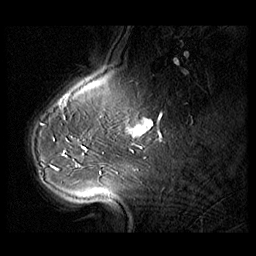
Breast MRI (dynamic contrast-enhanced), one sagittal slice. Position 26 of 104 along the scan axis. 3 images stored at this slice position (order not interpretable as contrast timing). 1.5 T. TE 1.3 ms, TR 5.5 ms. 3 mm slice thickness. 256 × 256 image matrix, field of view 220 × 220 mm. Patient: female, 54 years. Case-level facts recorded for this patient, not image findings: setting: breast cancer imaged before/during neoadjuvant chemotherapy; receptor status: HR-positive, HER2-negative.
Annotated regions visible in this slice (semi-automatically segmented with operator editing):
- analysis volume of interest (the breast-tissue region the enhancement analysis was run in; not a lesion): bounding box <28,127,104,182> (left, top, right, bottom; pixels)
- tumour enhancement mask (voxels above the 140 % enhancement threshold inside the analysis volume of interest): <83,147,85,149>